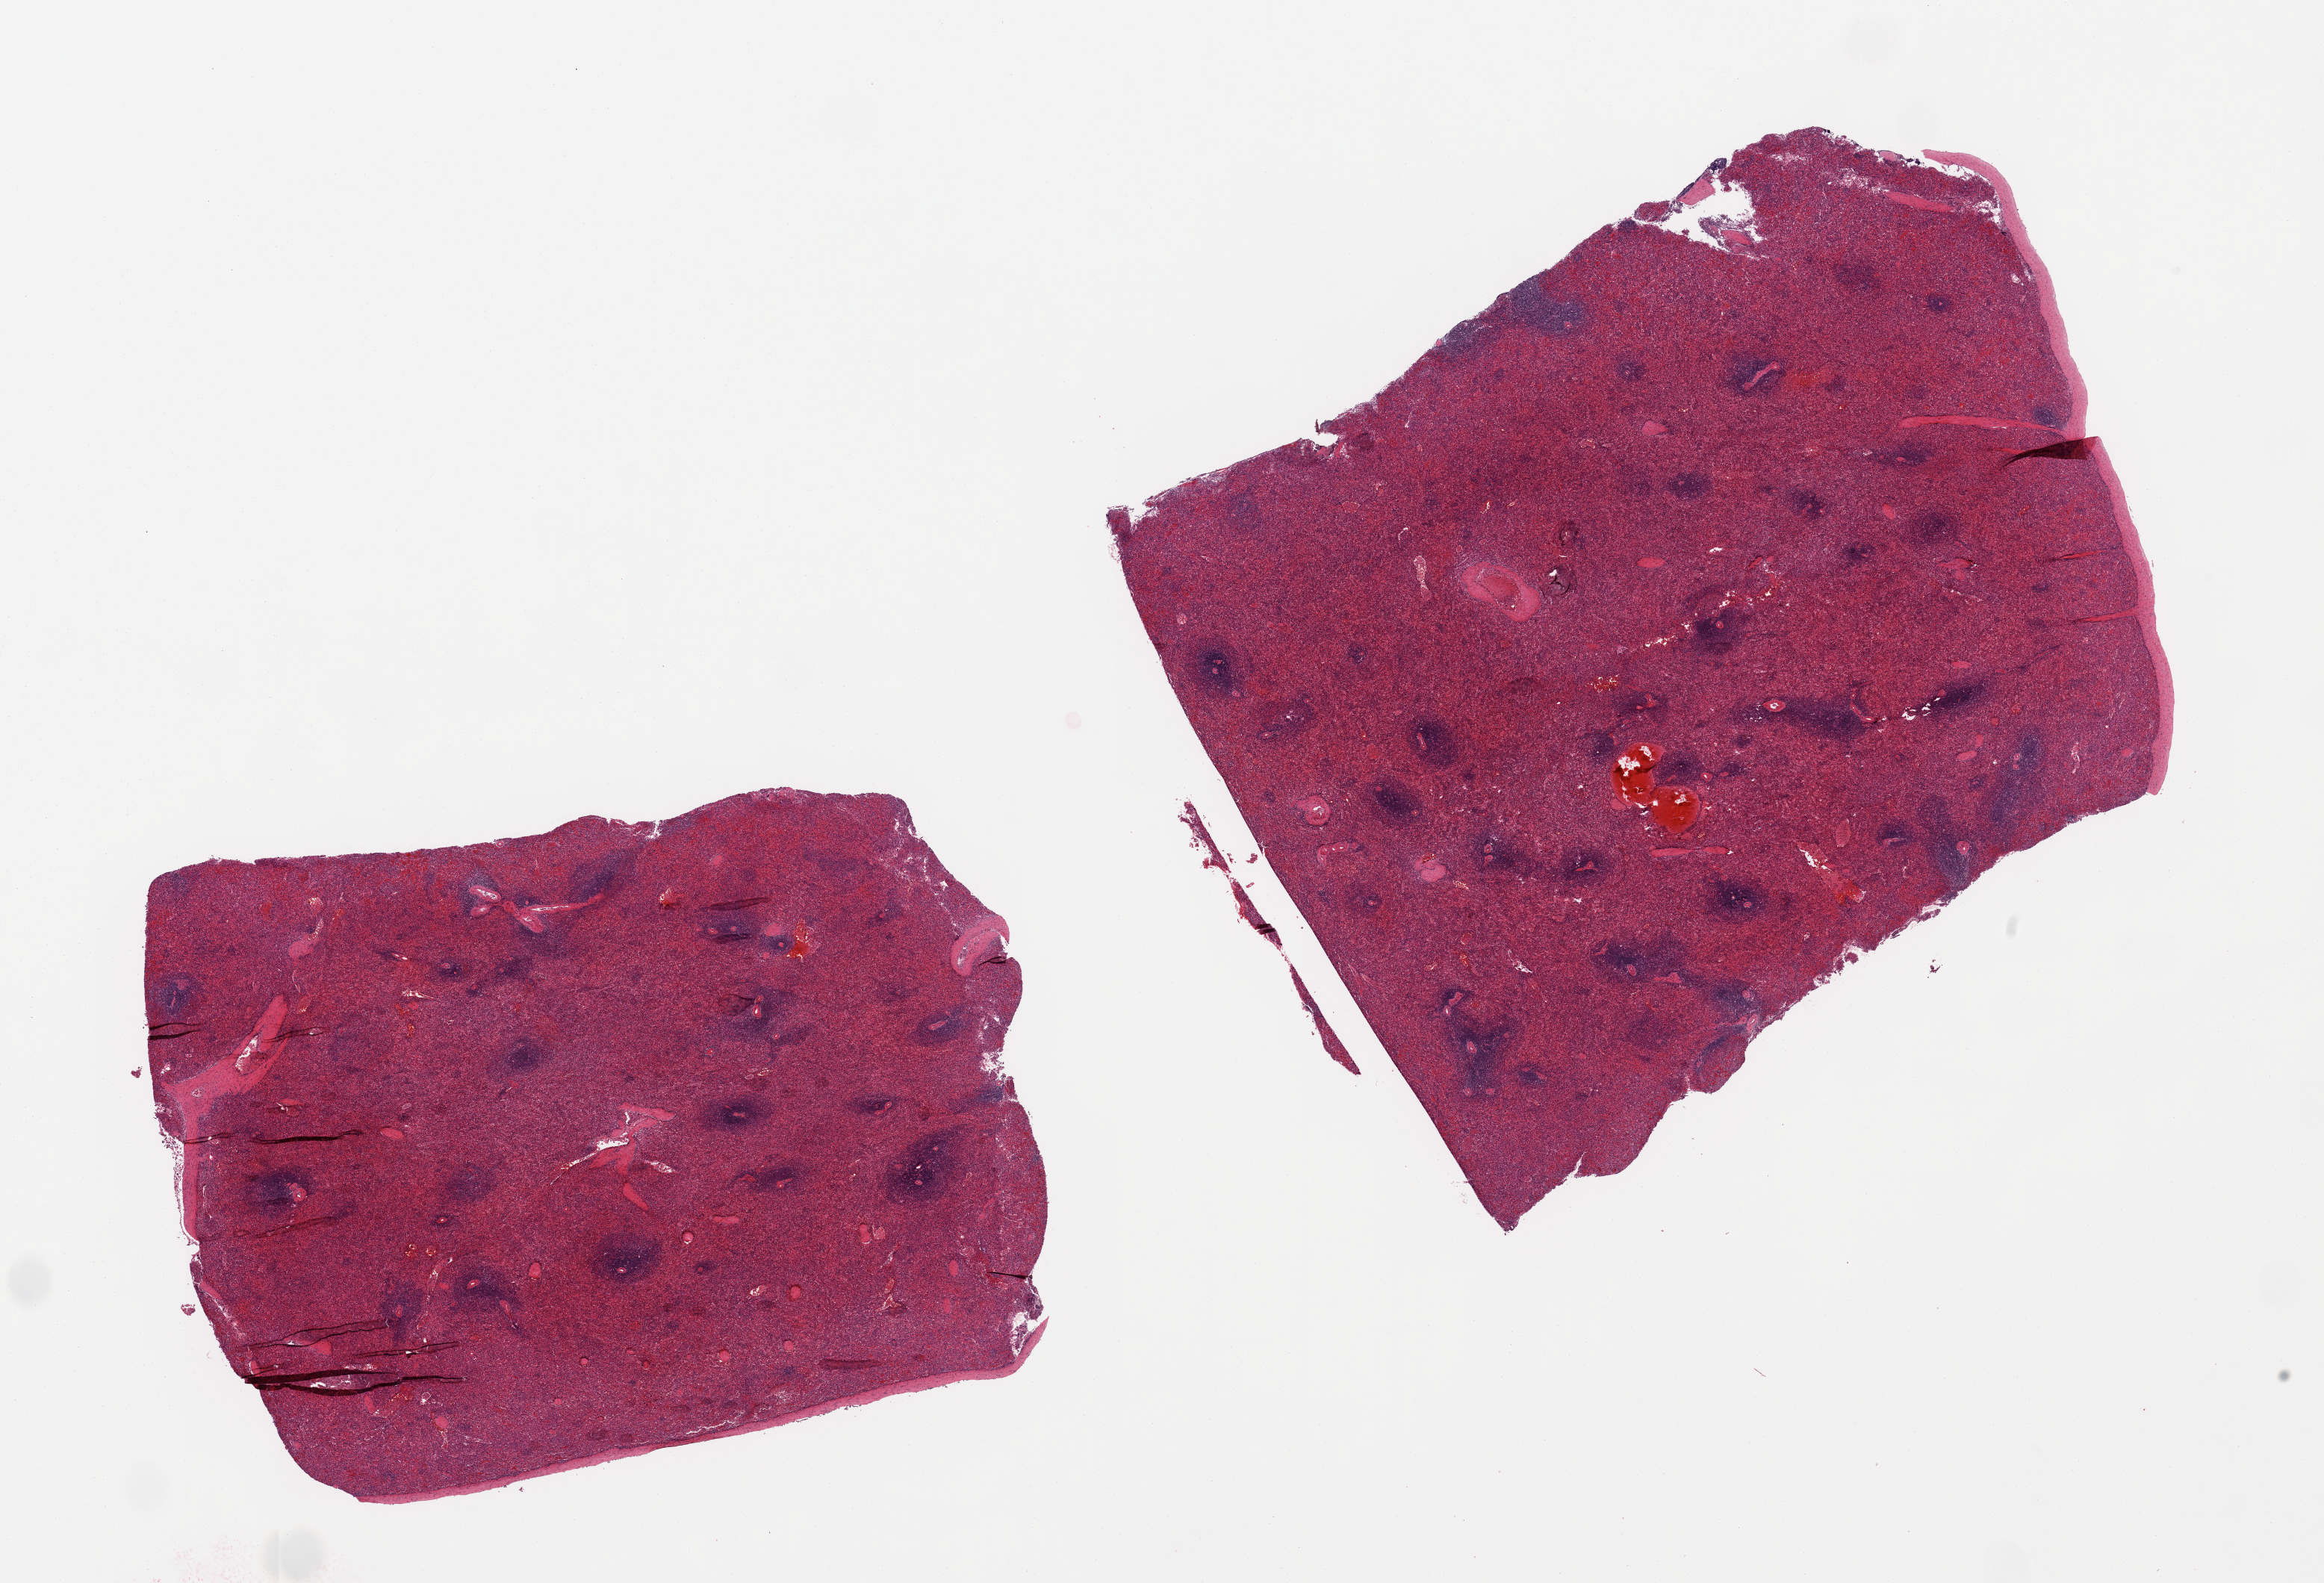
Whole-slide image, haematoxylin and eosin stain — shown as a low-resolution overview of the whole scanned area (about 24.6 x 16.8 mm, slide scanned at 20x); PAXgene-fixed, paraffin-embedded tissue; section of spleen (target tissue); tissue donor sample. Donor: male.
* reviewer comment on this tissue sample: 2 pieces, no abnormalities